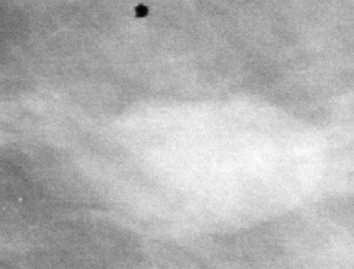
Crop from a digitized film mammogram around one marked abnormality, left breast, MLO view, BI-RADS breast density category 2 (scale 1–4).
Mass, shape oval, margins circumscribed; BI-RADS assessment category 3; pathology result (as recorded, not read from the image): benign.